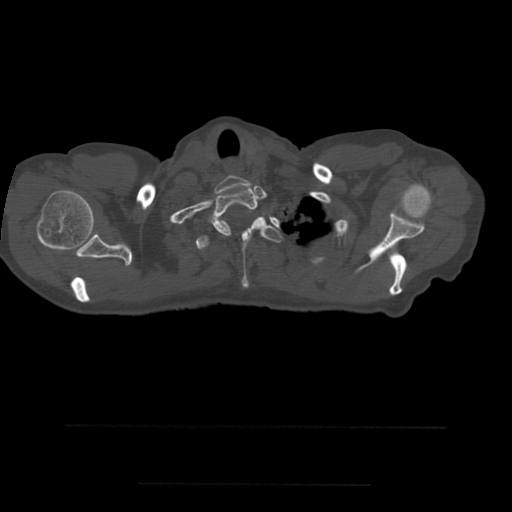
CT including the spine, one axial slice; position 442 of 544 along the scan axis; bone window (W 1800 / L 400 HU); 512 × 512 image matrix. Patient age 58 years. Case-level facts recorded for this patient, not image findings: primary cancer: lung.
Structures marked on this image (semi-automatically segmented with operator editing):
- T1 vertebra: bounding box (x1, y1, x2, y2) in pixels: (194, 186, 258, 236)
- T2 vertebra: (196, 217, 284, 288)